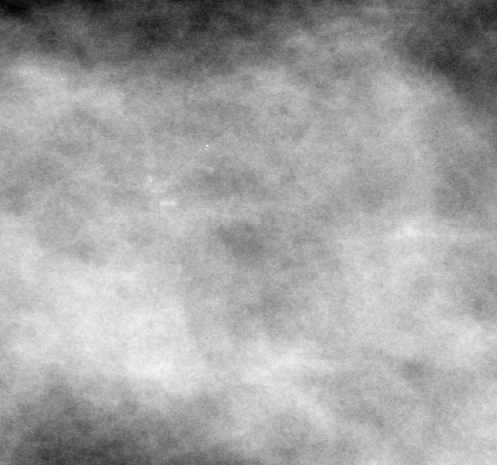
Crop from a digitized film mammogram around one marked abnormality, left breast, CC view, BI-RADS breast density category 3 (scale 1–4).
Calcifications, morphology amorphous, distribution clustered; BI-RADS assessment category 4; pathology result (as recorded, not read from the image): benign.